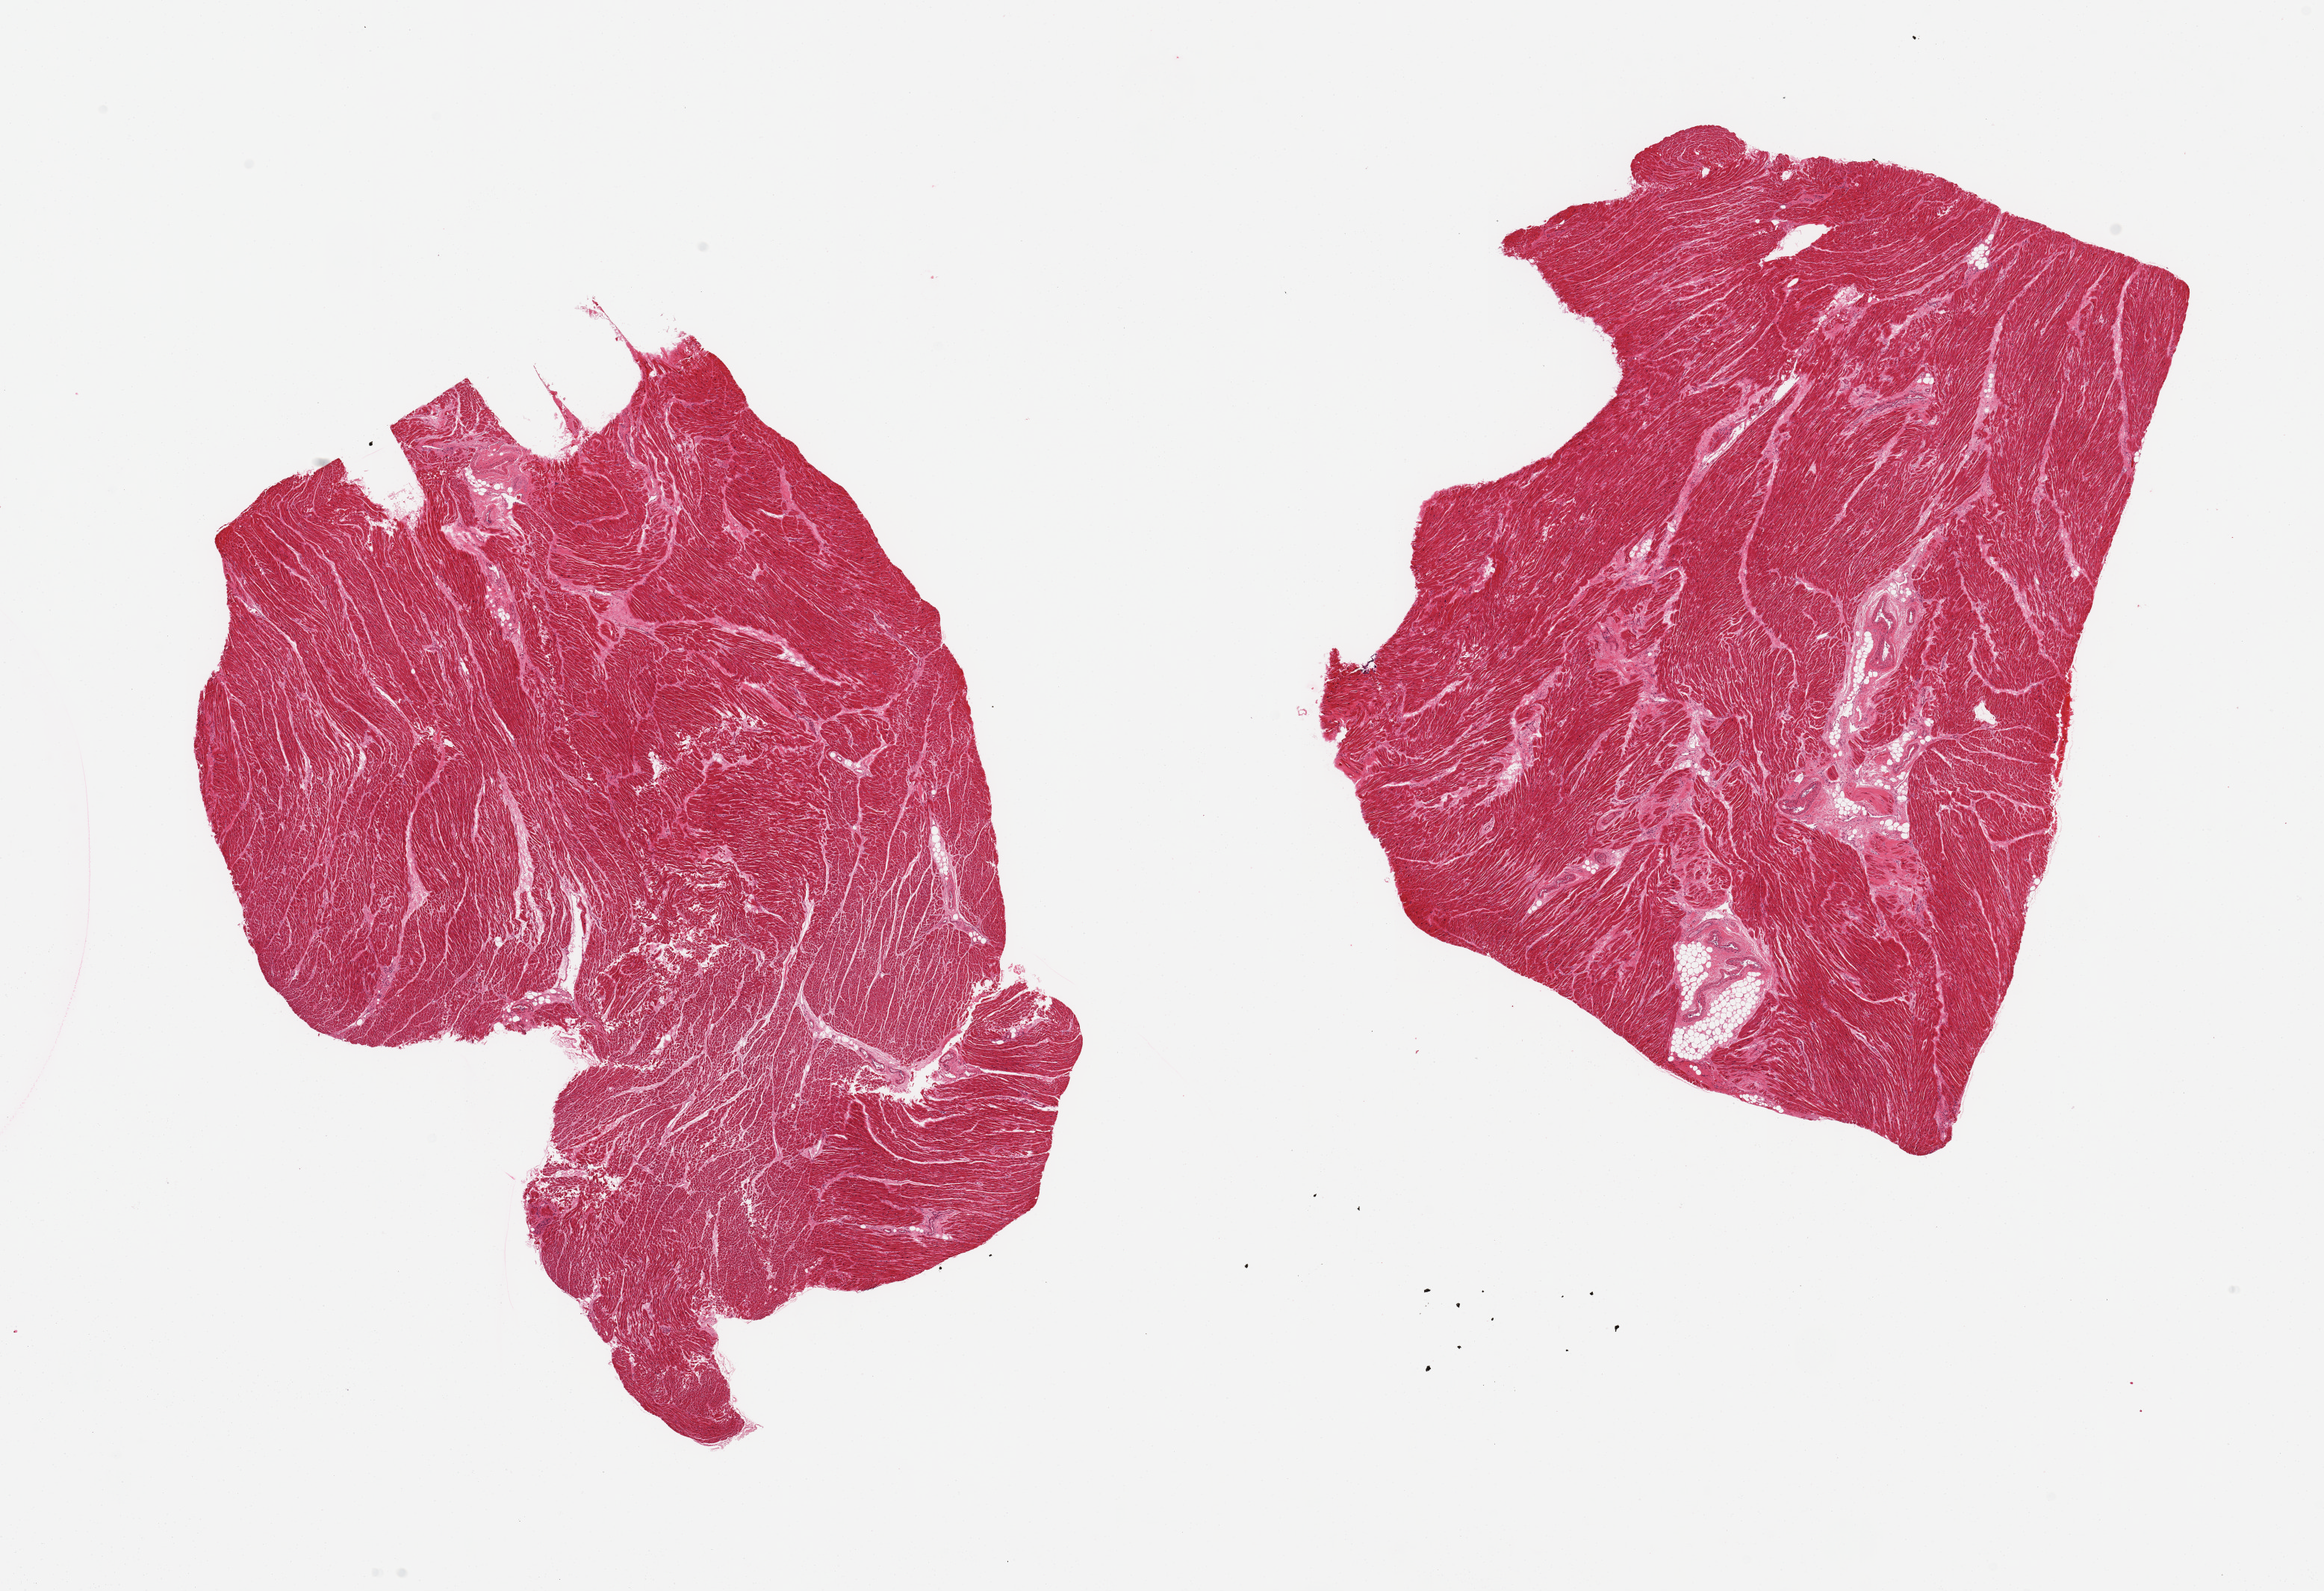
Whole-slide image, hematoxylin and eosin (H&E) stain, shown as a low-resolution overview of the whole scanned area (about 24.6 x 16.8 mm); PAXgene-fixed paraffin-embedded (PFPE) section; target tissue: heart; donor tissue sample. Male donor.
Pathologist's review note for this sample: 2 pieces; some interstitial fibrosis and few boxcar nuclei suggesting myocyte hypertrophy.